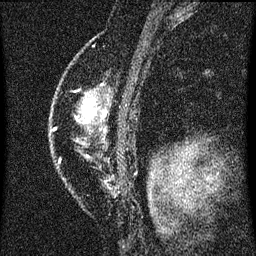
Breast MRI (dynamic contrast-enhanced), one sagittal slice. Dynamic contrast-enhanced series, image 2 of 3 at this slice position (ordered by acquisition). 1.5 T. TE 4.2 ms, TR 8 ms. 2 mm slice thickness. 256 × 256 image matrix, field of view 180 × 180 mm. Patient: female, 46 years.
Annotated regions visible in this slice (semi-automatic segmentation, software-assisted and operator-edited):
- analysis volume of interest (the breast-tissue region the enhancement analysis was run in; not a lesion): bounding box (x1, y1, x2, y2) in pixels: (58, 86, 110, 187)
- tumour enhancement mask (voxels above the 70 % enhancement threshold inside the analysis volume of interest): (83, 100, 95, 115)